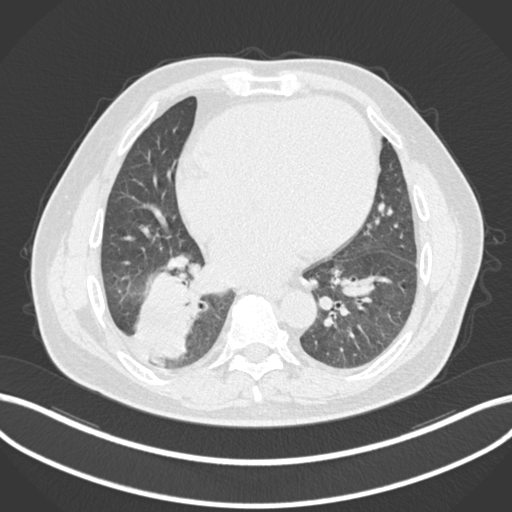
Chest CT, one axial slice; slice 62 of 200 in the series (ordered by position); reconstruction kernel B30f; 120 kVp; lung window (W 1500 / L -600 HU); 512 × 512 image matrix. Male patient, age 59 years.
Structures marked on this image (bounding box drawn by a radiologist):
- lung tumour (recorded histology: adenocarcinoma): bounding box <138,271,196,361> (left, top, right, bottom; pixels)